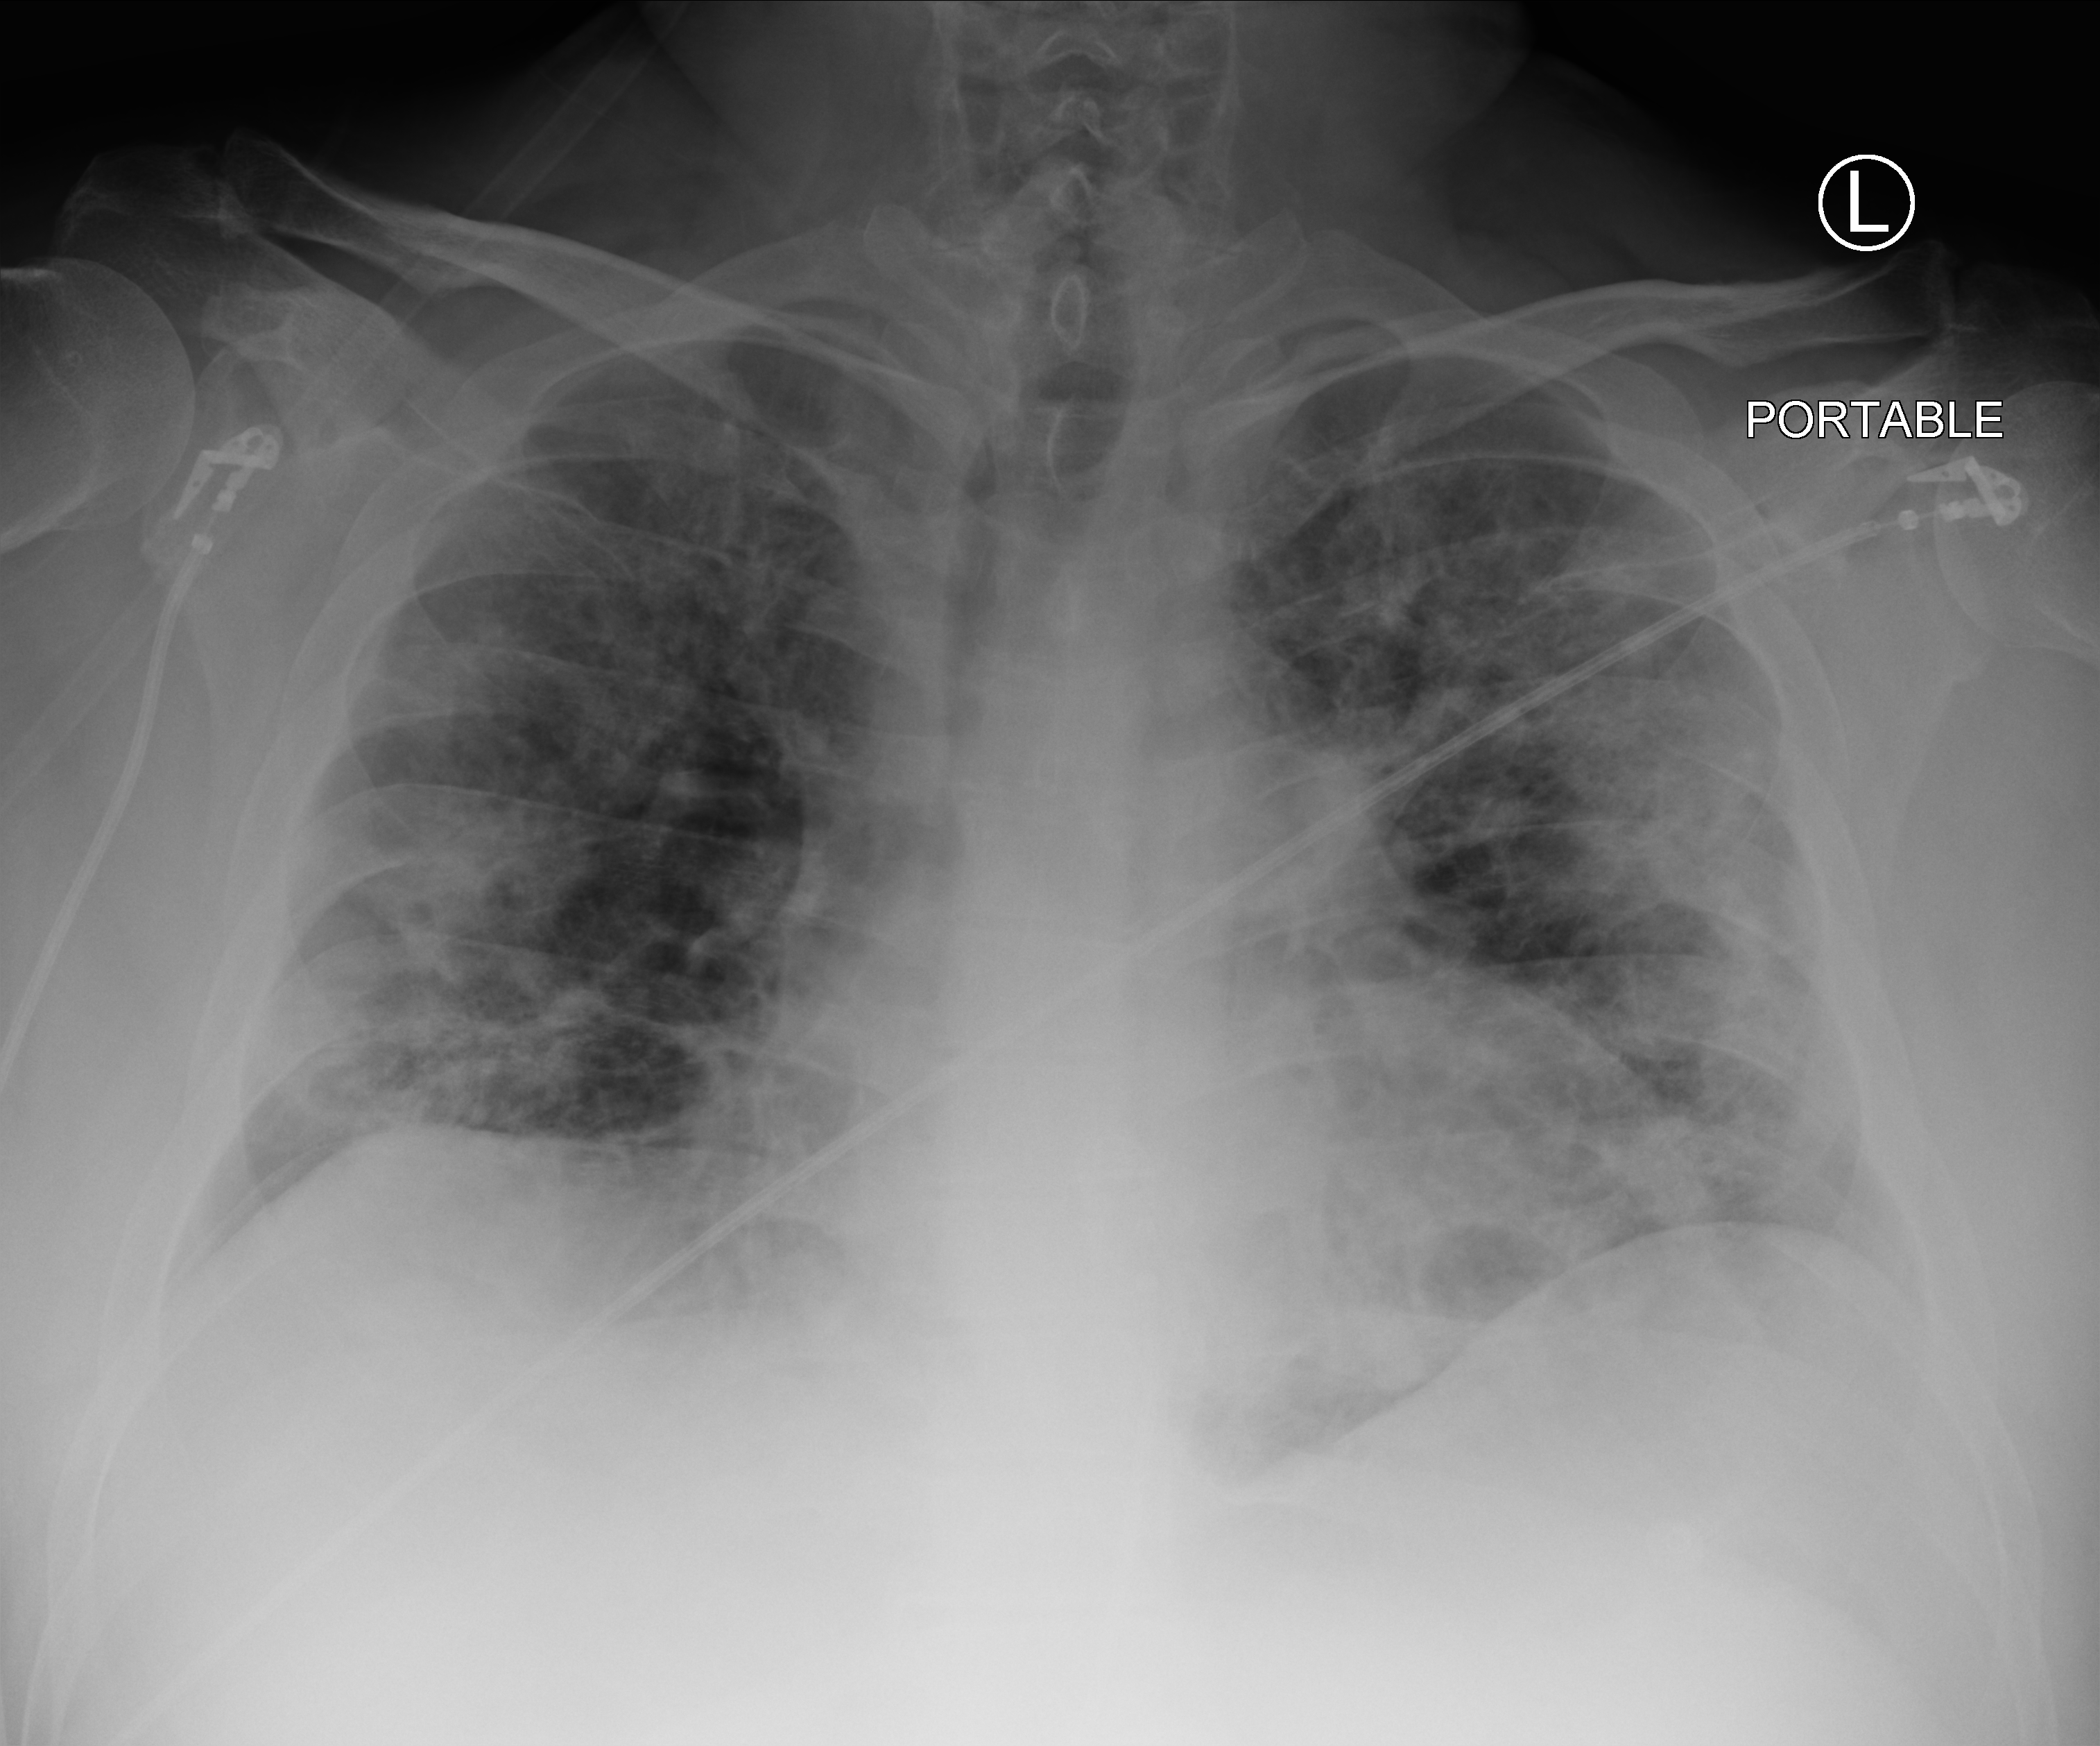
Bedside chest radiograph (computed radiography), anteroposterior (AP) projection. Patient hospitalised with COVID-19; male, aged 18–59 years.
Admission-level facts for this patient (not findings on this image; timing relative to this image not recorded): mechanically ventilated during this hospital stay: no; chronic kidney disease (admission record): no.